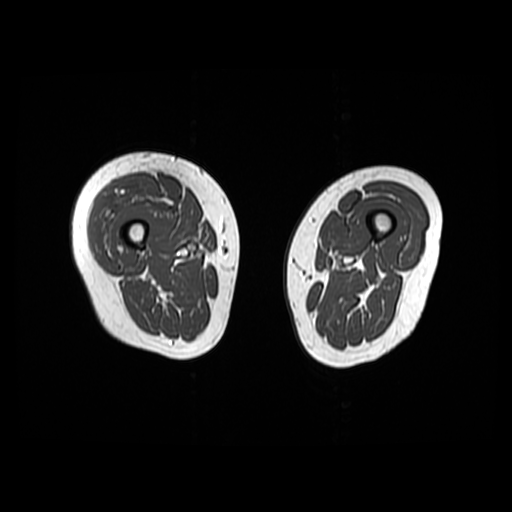
MRI of an extremity soft-tissue mass, one axial slice; position 16 of 48 along the scan axis; 6 mm slice thickness; 512 × 512 image matrix, field of view 440 × 440 mm. Female patient. Case-level facts recorded for this patient, not image findings: histological type: pleiomorphic undifferentiated sarcoma; grade: high; site of the primary tumour: right quadricep.
Structures marked on this image (manually delineated by an expert):
- gross tumour volume including surrounding oedema: bounding box (x1, y1, x2, y2) in pixels: (92, 182, 160, 256)